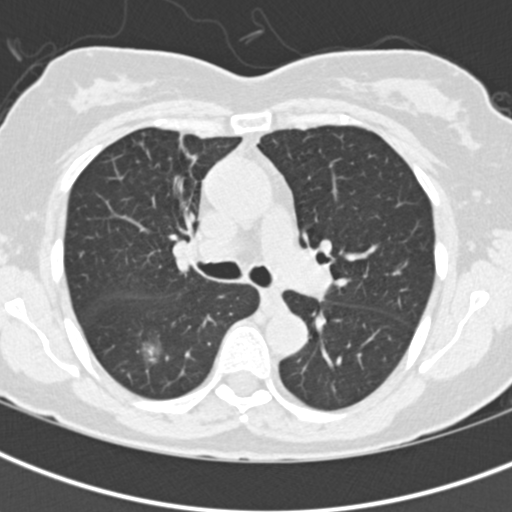
Low-dose screening chest CT, one axial slice; slice 134 of 198 in the series (ordered by position); lung window (W 1500 / L -600 HU); 2 mm slice thickness; 512 × 512 image matrix, field of view 290 × 290 mm.
Structures marked on this image (outlined manually by an expert reader):
- lesion 1 (tumor, lower lobe of right lung): bounding box (x1, y1, x2, y2) in pixels: (142, 341, 162, 366)